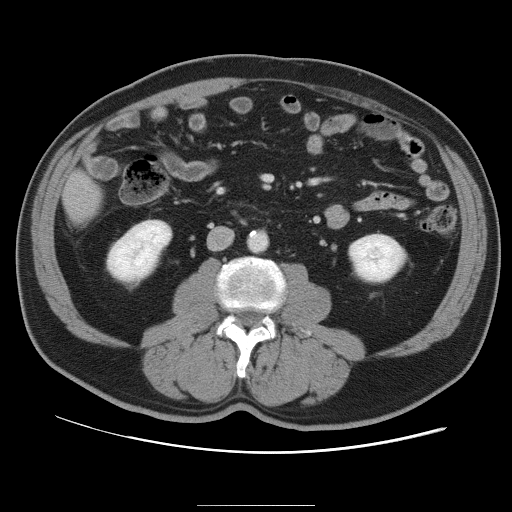
Contrast-enhanced abdominal CT, one axial slice. 120 kVp. Soft-tissue window (W 400 / L 40 HU). 5 mm slice thickness. 512 × 512 image matrix. Male patient, age 64 years. From the clinical record (not read from this slice): diagnosis: colorectal cancer liver metastases, imaged before liver resection; multiple liver metastases: yes; largest metastasis: 3 cm; disease in both lobes: yes.
Structures marked on this image (expert manual segmentation):
- liver: bounding box <66,173,101,218> (left, top, right, bottom; pixels)
- planned liver remnant (the part of the liver to remain after resection): <65,174,102,218>